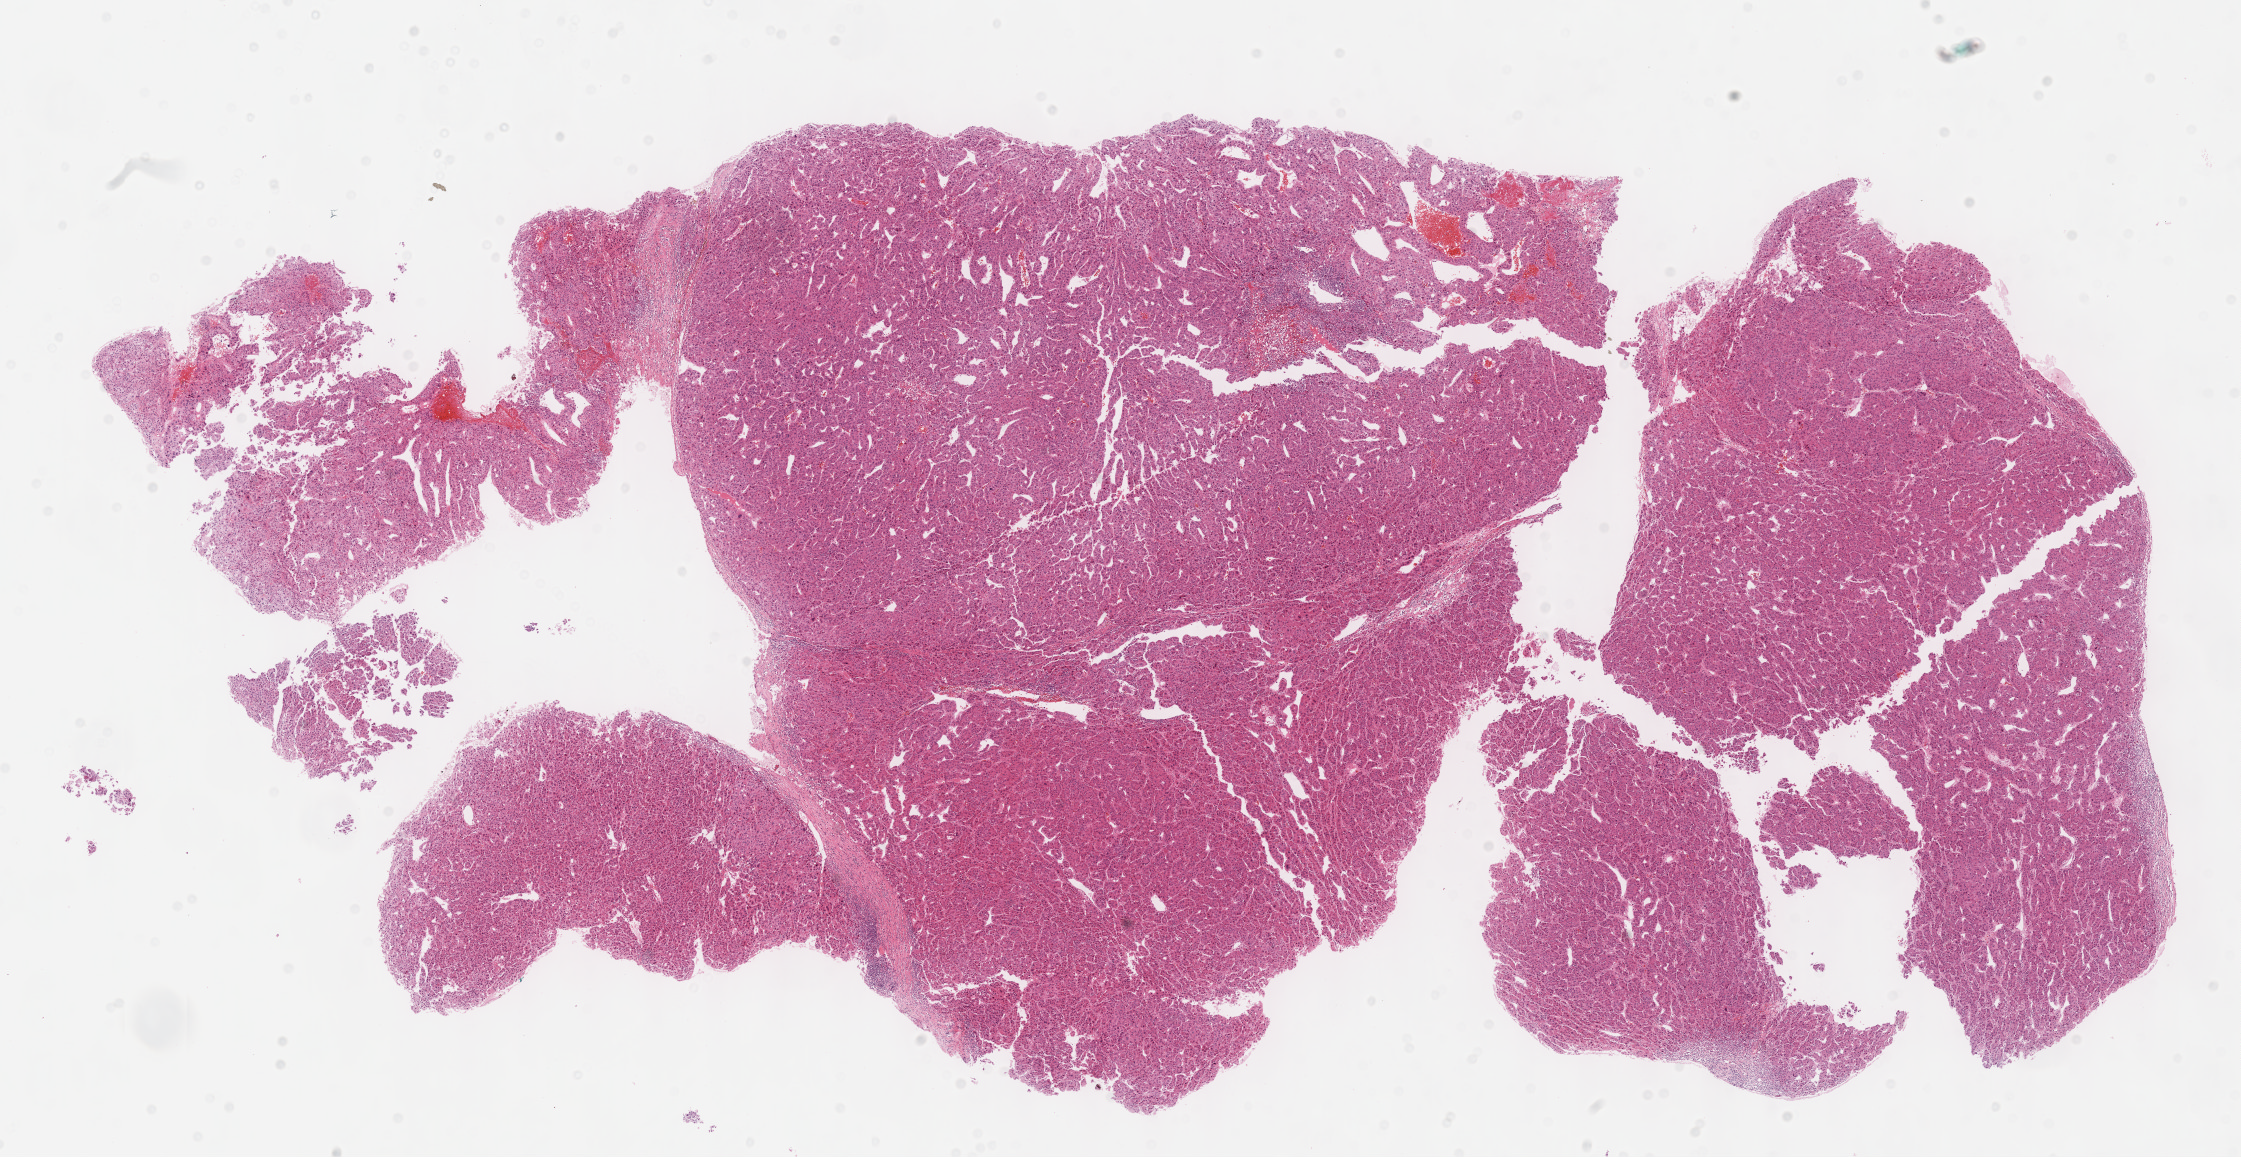
Whole-slide histology image, H&E-stained, a low-resolution overview of the entire scanned area, about 18.1 x 9.3 mm (slide scanned at 40x); FFPE section; sample: primary tumour, liver. Male, age 59 years at initial diagnosis. Histologic grade: G3 (poorly differentiated).
AJCC pathologic stage: II (7th edition). Pathologic diagnosis: Hepatocellular carcinoma, NOS.